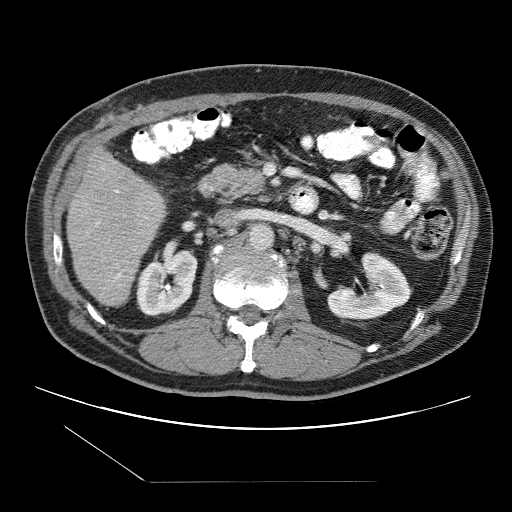
Contrast-enhanced abdominal CT (liver protocol), one axial slice. Position 35 of 109 along the scan axis. Reconstruction kernel STANDARD. 120 kVp. One of 2 acquisitions stored at this slice position. Soft-tissue window (W 400 / L 40 HU). 2.5 mm slice thickness. 512 × 512 image matrix, field of view 400 × 400 mm. From the clinical record (not read from this slice): diagnosis: hepatocellular carcinoma (patient treated with transarterial chemoembolisation; whether this scan precedes or follows treatment is not stated here); TNM stage (as recorded): Stage-IIIB; Child-Pugh class: A; tumour nodularity: multinodular.
Annotated regions visible in this slice (semi-automatic segmentation, software-assisted and operator-edited):
- liver parenchyma outside the tumour (the mass and vessels are separate outlines, so this box may not span the whole liver): box from (x=66, y=148) to (x=165, y=306) px
- liver vessels: (x=96, y=168)–(x=121, y=279)